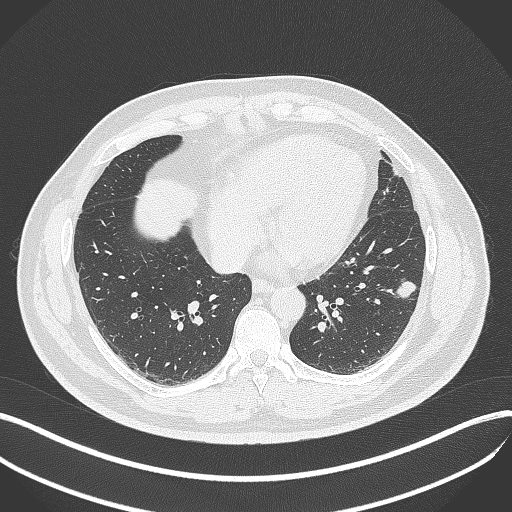
Chest CT, one axial slice. Slice 152 of 429 in the series (ordered by position). Lung window (W 1500 / L -600 HU). 1 mm slice thickness. 512 × 512 image matrix, field of view 400 × 400 mm. Patient: male, 39 years. From the clinical record (not read from this slice): clinical TNM (as recorded): T2a N0 M0; histopathological grade: G2-3.
Outlined on this slice (bounding box drawn by a radiologist):
- lung tumour (recorded histology: adenocarcinoma): bounding box [x1, y1, x2, y2] px = [390, 274, 422, 303]